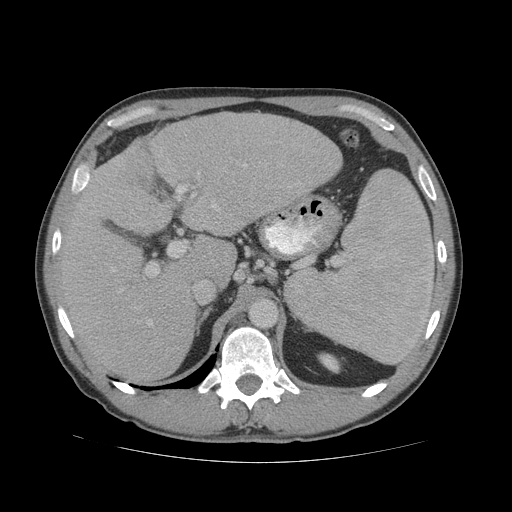
Contrast-enhanced abdominal CT (liver protocol), one axial slice; slice 42 of 81 in the series (ordered by position); 140 kVp; soft-tissue window (W 400 / L 40 HU); 2.5 mm slice thickness; 512 × 512 image matrix, field of view 400 × 400 mm. From the clinical record (not read from this slice): diagnosis: hepatocellular carcinoma (patient treated with transarterial chemoembolisation; whether this scan precedes or follows treatment is not stated here); TNM stage (as recorded): Stage-IVB; Child-Pugh class: B.
Annotated regions visible in this slice (semi-automatically segmented with operator editing):
- liver parenchyma outside the tumour (the mass and vessels are separate outlines, so this box may not span the whole liver): box from (x=54, y=112) to (x=342, y=382) px
- mass: (x=115, y=147)–(x=154, y=189)
- liver vessels: (x=111, y=164)–(x=290, y=326)